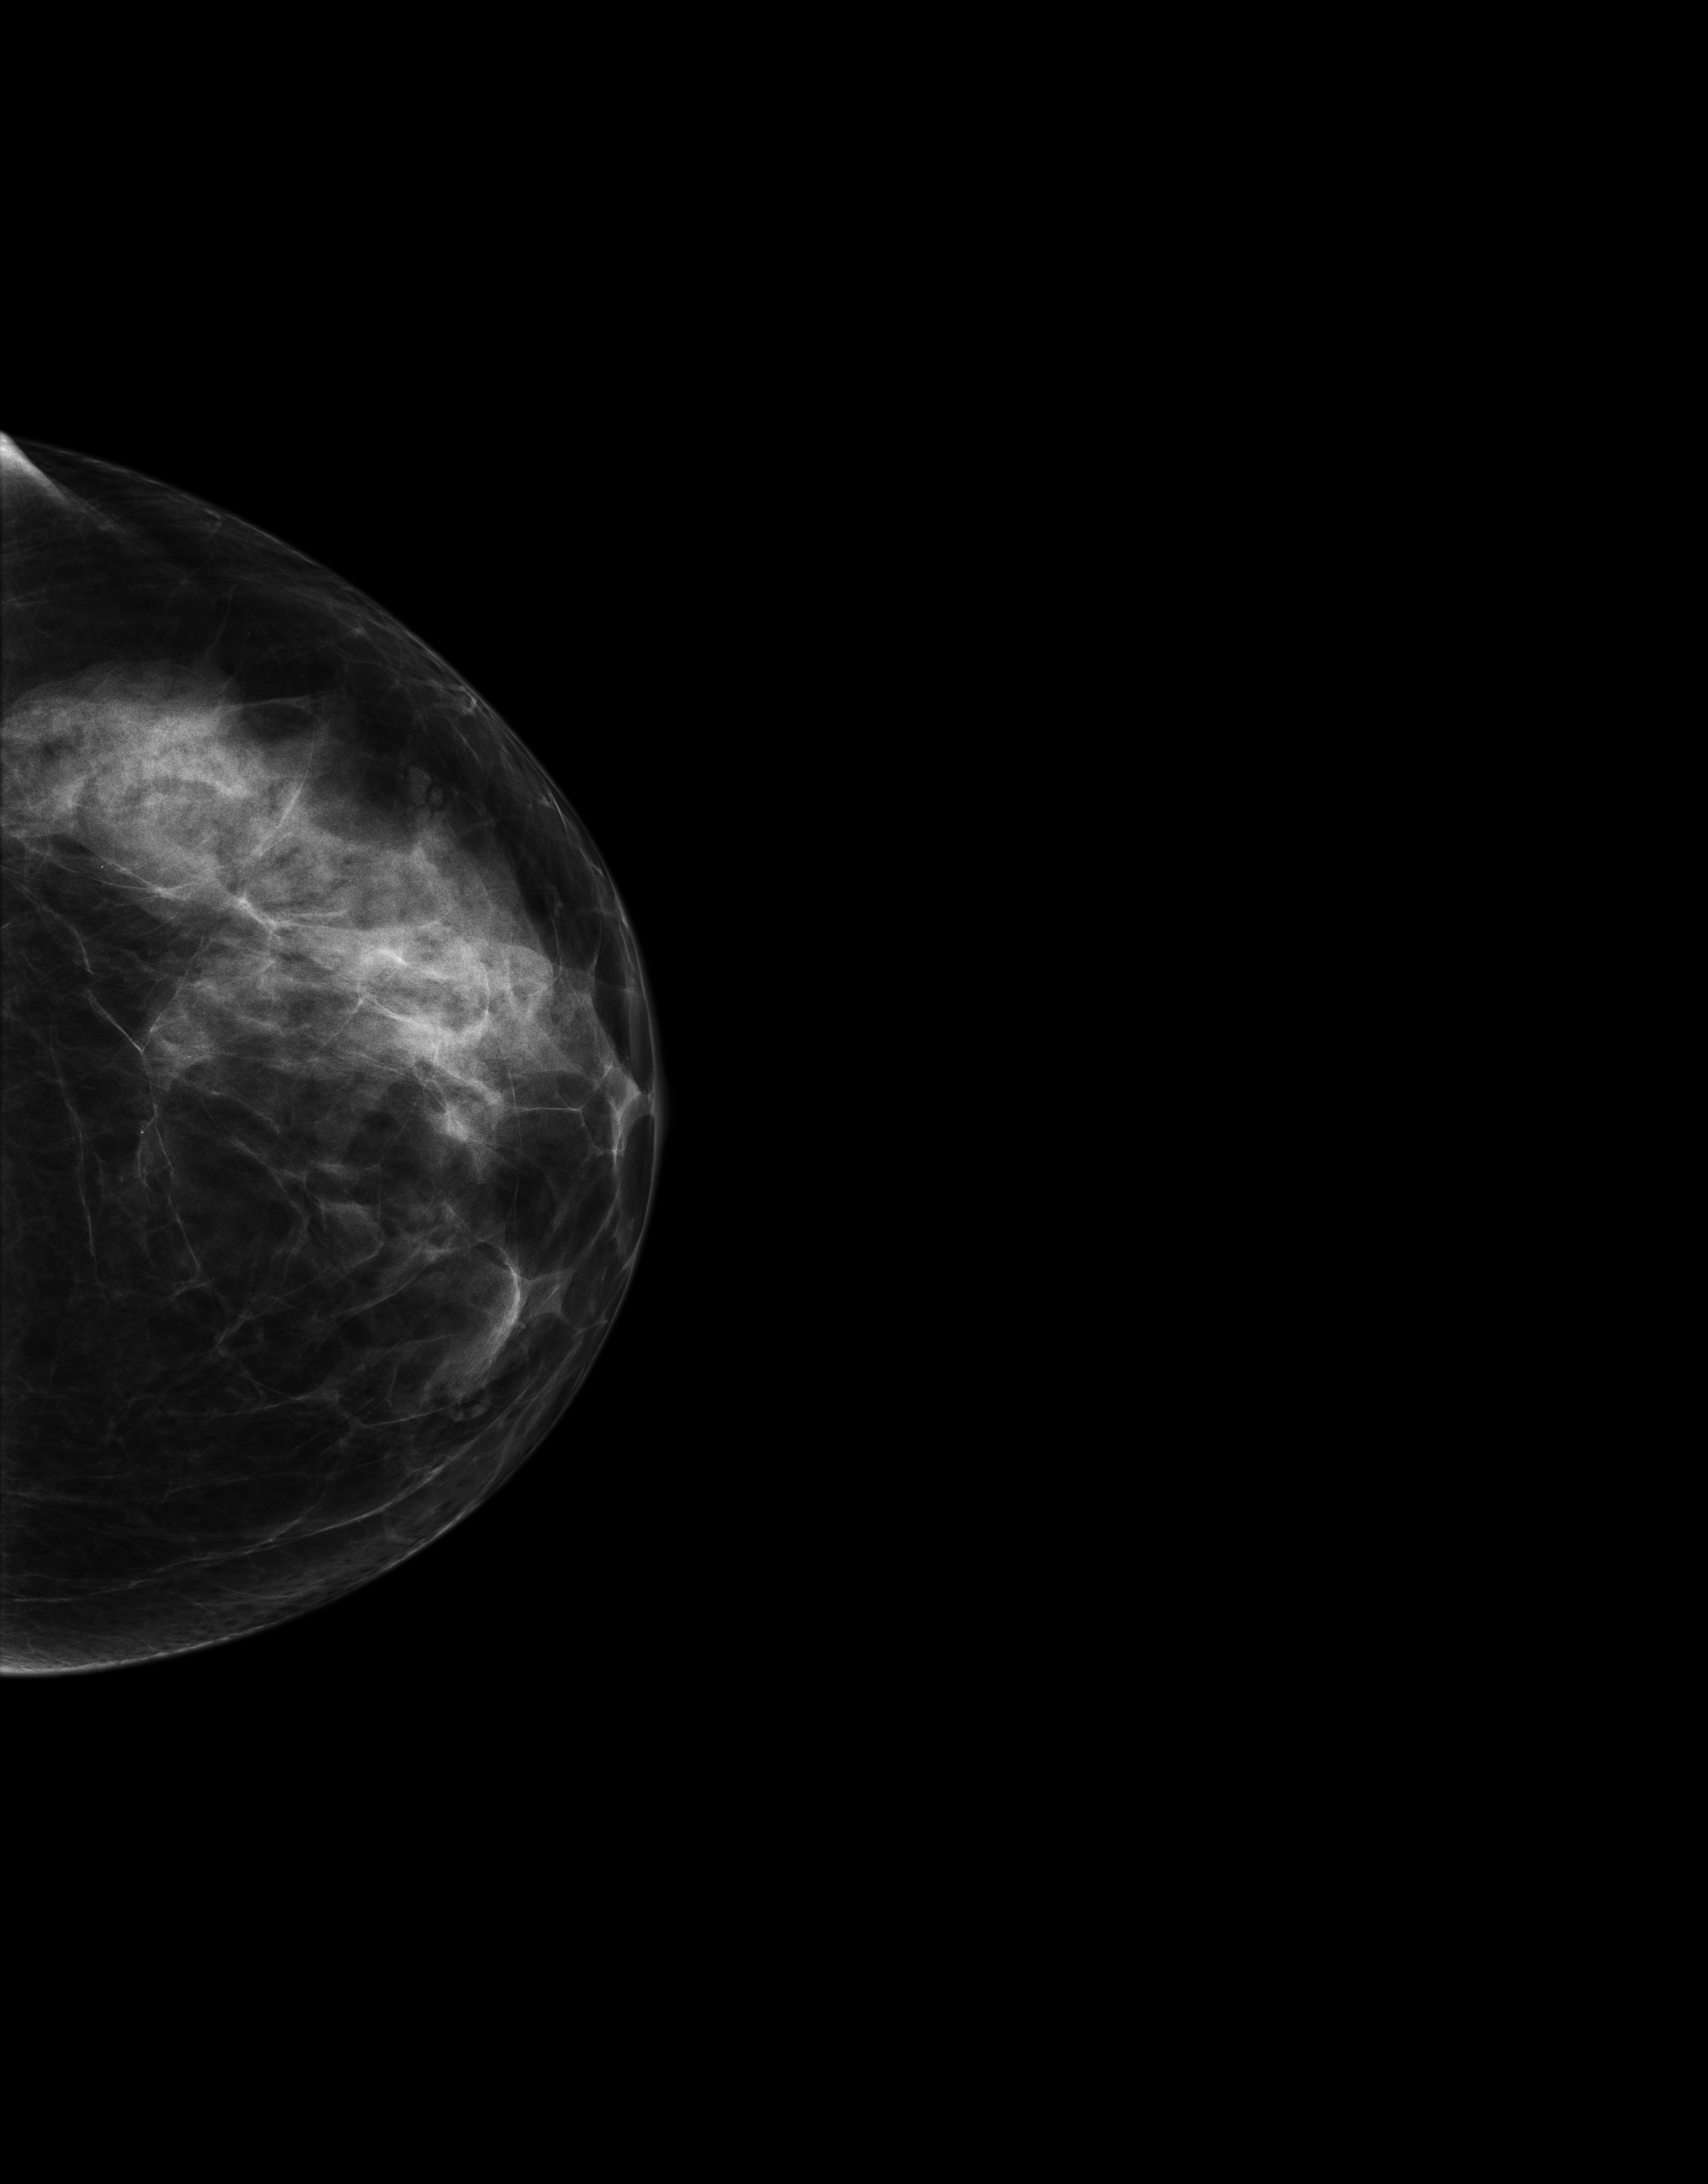
Screening examination, compressed breast thickness 54 mm. Female patient, age 52 years.
Image type: full-field digital mammogram. Breast: left. Projection: CC view.